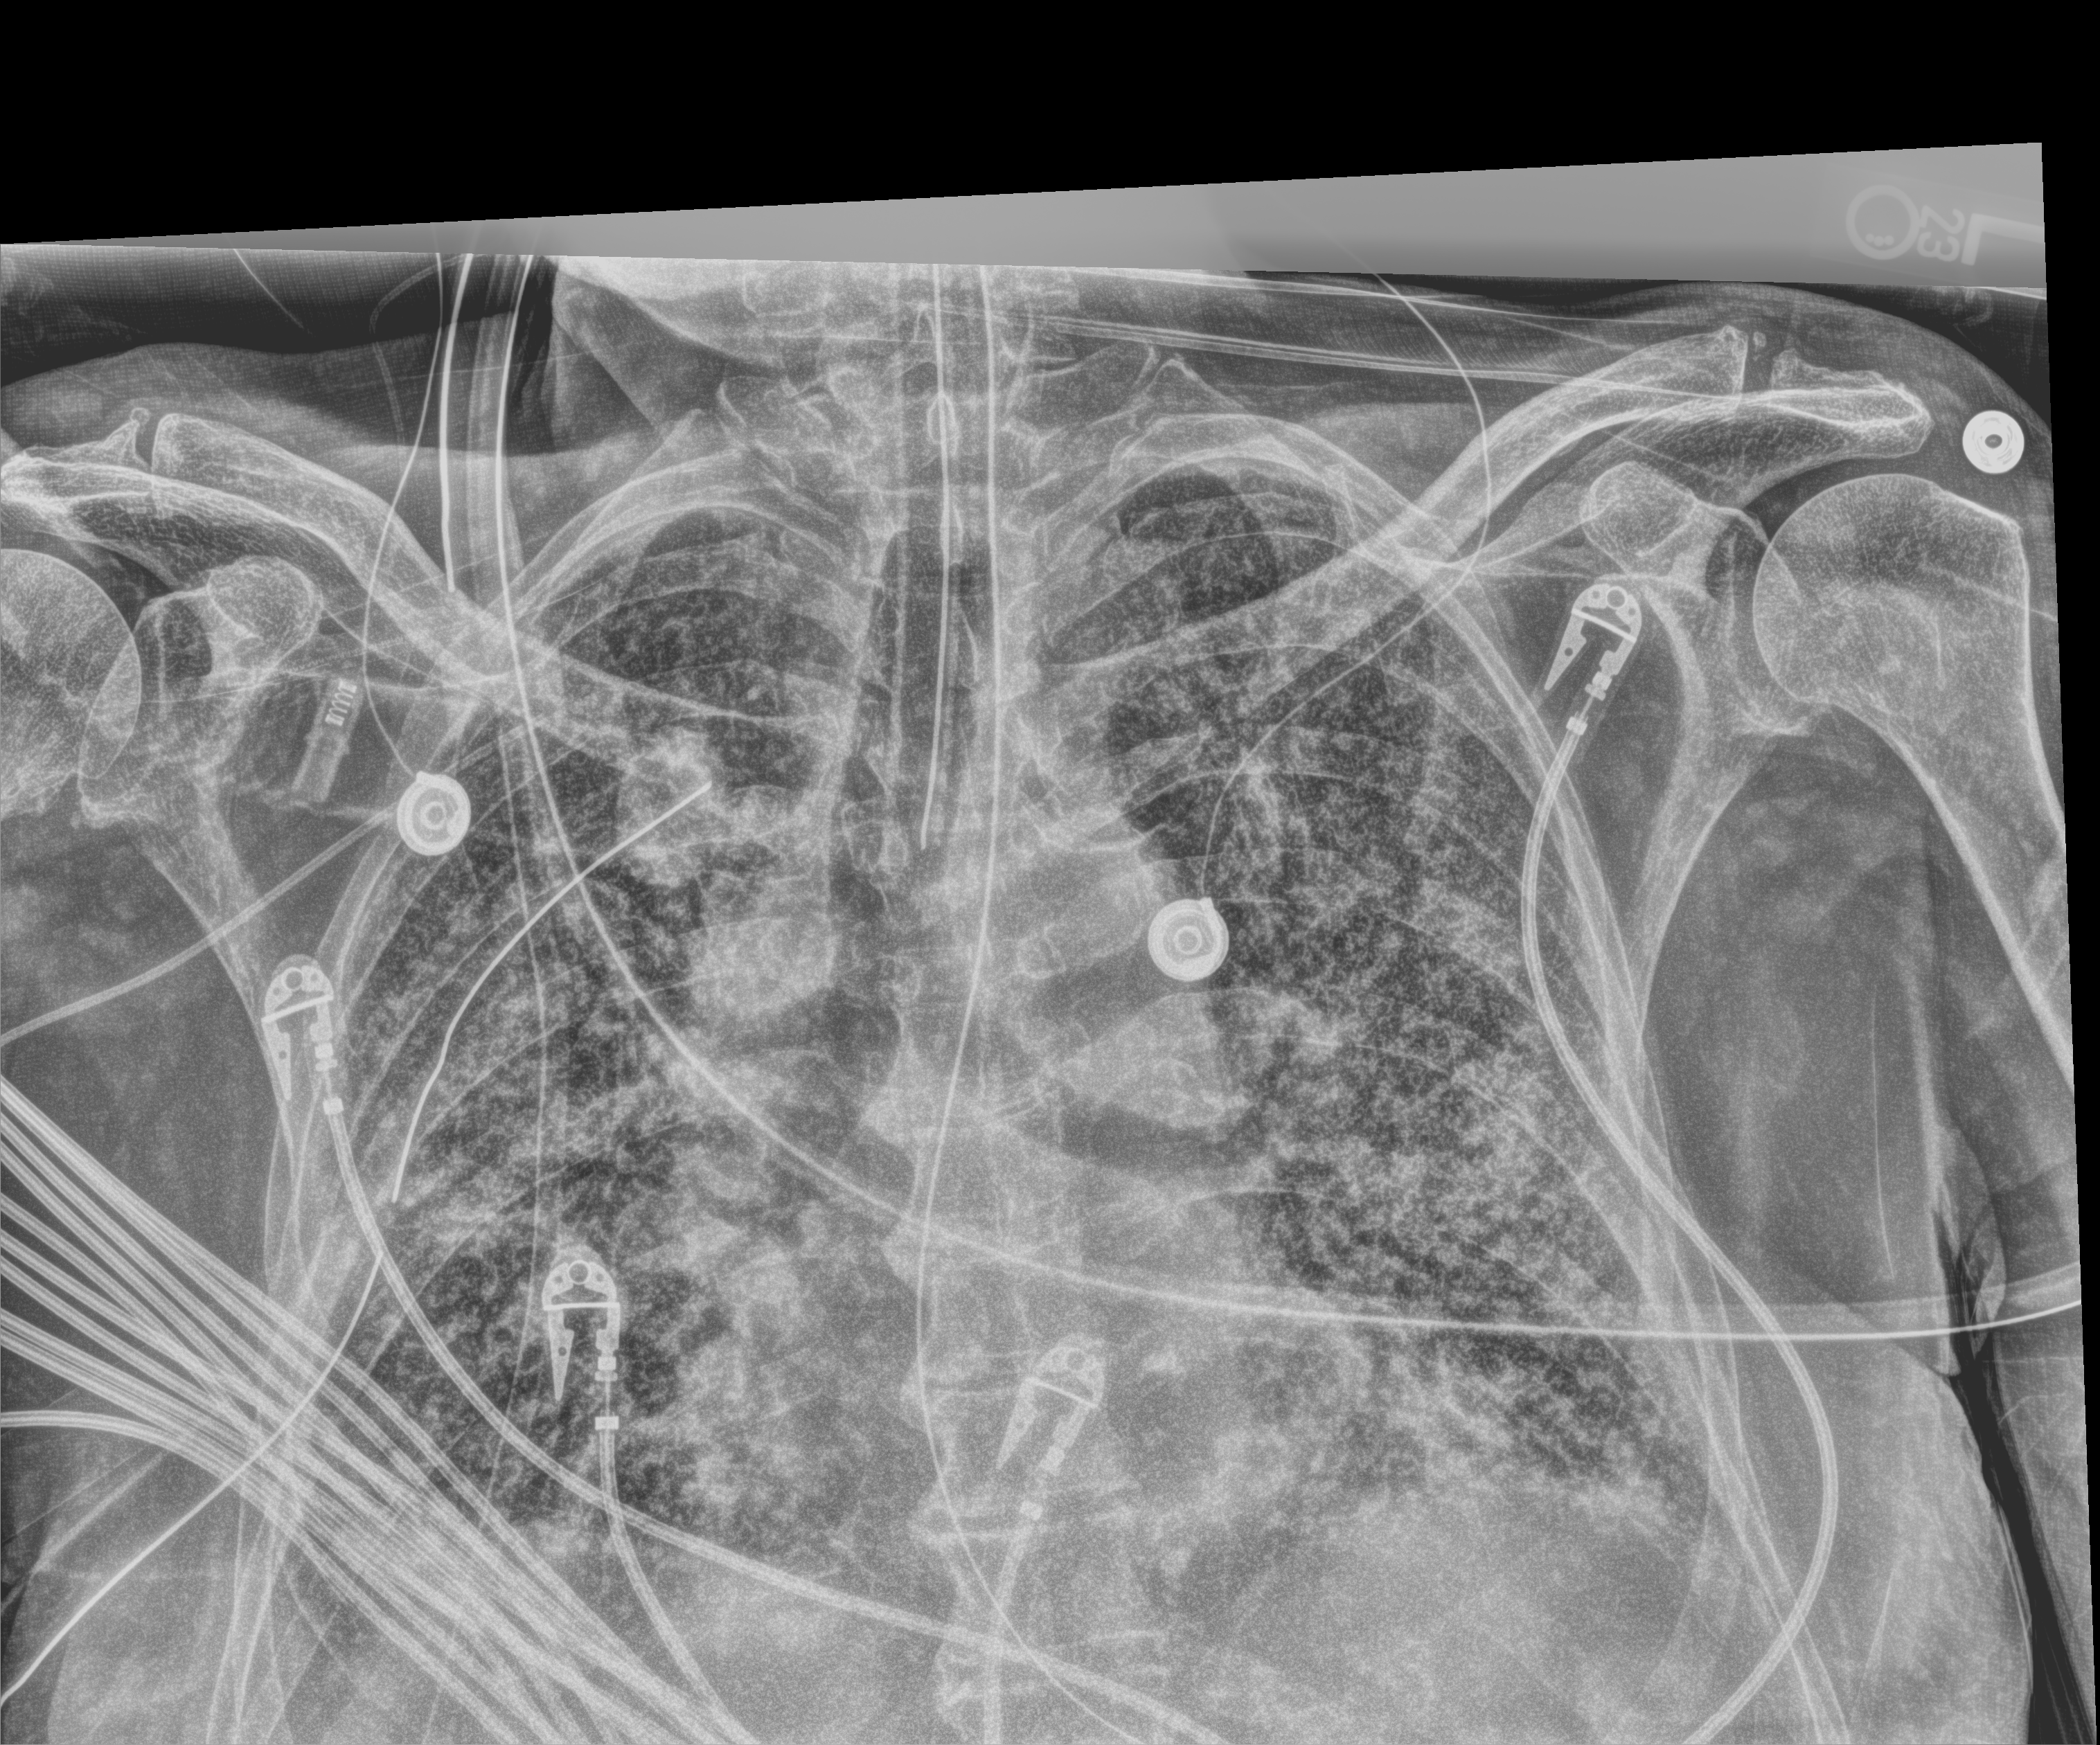
Chest X-ray (portable). Male patient hospitalised with COVID-19, age 75–90 years.
Hospital-stay facts (about this admission, not read from this image; timing relative to this image not recorded): admitted to intensive care during this hospital stay: yes.